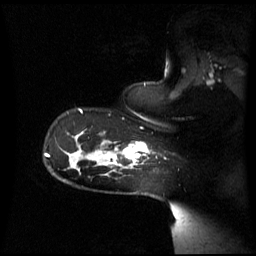
Breast MRI (dynamic contrast-enhanced), one sagittal slice; dynamic contrast-enhanced series, image 2 of 3 at this slice position (ordered by acquisition); 1.5 T; TE 4.2 ms, TR 8.4 ms; 2.8 mm slice thickness; 256 × 256 image matrix. Patient: female, 39 years. Case-level facts recorded for this patient, not image findings: setting: breast cancer imaged before/during neoadjuvant chemotherapy; receptor status: triple-negative.
Annotated regions visible in this slice (semi-automatic segmentation, software-assisted and operator-edited):
- analysis volume of interest (the breast-tissue region the enhancement analysis was run in; not a lesion): bounding box (x1, y1, x2, y2) in pixels: (101, 132, 149, 172)
- tumour enhancement mask (voxels above the 70 % enhancement threshold inside the analysis volume of interest): (105, 143, 148, 164)